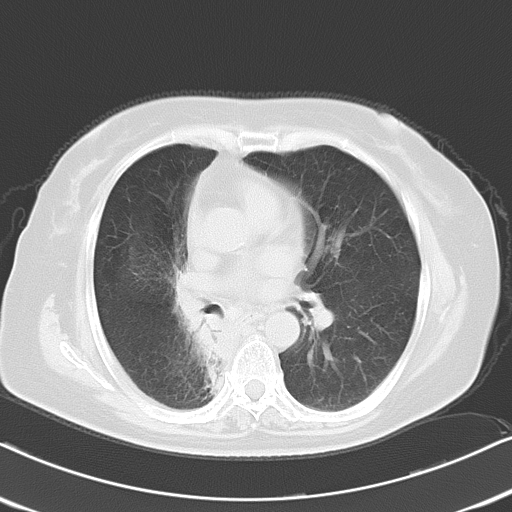
Chest CT, one axial slice. Position 11 of 21 along the scan axis. Reconstruction kernel B70f. 120 kVp. Lung window (W 1500 / L -600 HU). 10 mm slice thickness. 512 × 512 image matrix. Patient: female, 61 years. Case-level facts recorded for this patient, not image findings: clinical TNM (as recorded): T1b N0 M1b.
Annotated regions visible in this slice (bounding box drawn by a radiologist):
- lung tumour (recorded histology: squamous cell carcinoma): bounding box [x1, y1, x2, y2] px = [182, 276, 247, 409]